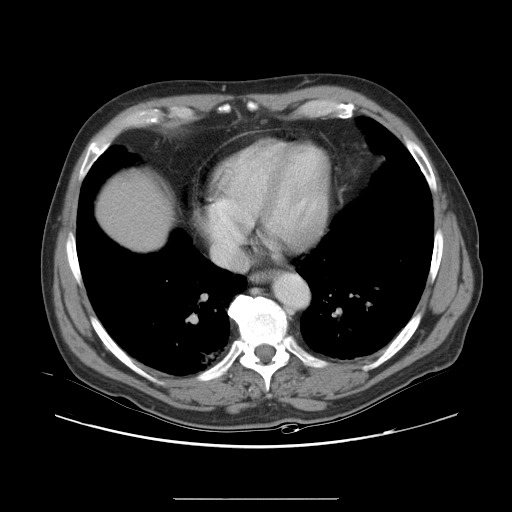
Contrast-enhanced abdominal CT, one axial slice; position 32 of 40 along the scan axis; 120 kVp; intravenous contrast given; soft-tissue window (W 400 / L 40 HU); 512 × 512 image matrix, field of view 408 × 408 mm. Male patient, age 64 years. From the clinical record (not read from this slice): diagnosis: colorectal cancer liver metastases, imaged before liver resection; multiple liver metastases: yes; largest metastasis: 3.2 cm; disease in both lobes: yes.
Outlined on this slice (outlined manually by an expert reader):
- liver: bounding box <100,175,166,249> (left, top, right, bottom; pixels)
- planned liver remnant (the part of the liver to remain after resection): <100,175,167,250>